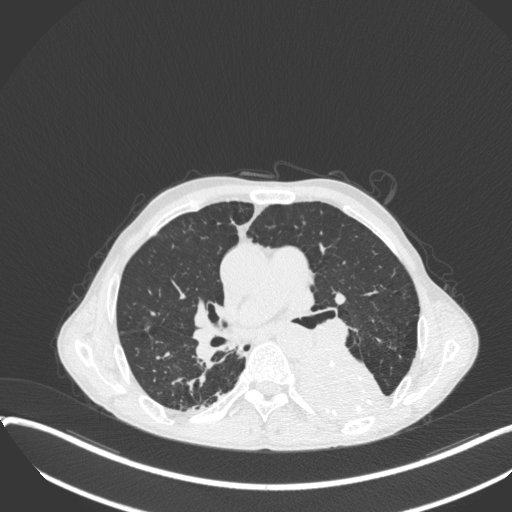
Chest CT, one axial slice. Slice 213 of 400 in the series (ordered by position). 120 kVp. Lung window (W 1500 / L -600 HU). 1 mm slice thickness. 512 × 512 image matrix, field of view 400 × 400 mm. Patient: male, 57 years. Case-level facts recorded for this patient, not image findings: clinical TNM (as recorded): T4 N0 M0.
Outlined on this slice (bounding box drawn by a radiologist):
- lung tumour (recorded histology: squamous cell carcinoma): bounding box [x1, y1, x2, y2] px = [294, 339, 394, 432]